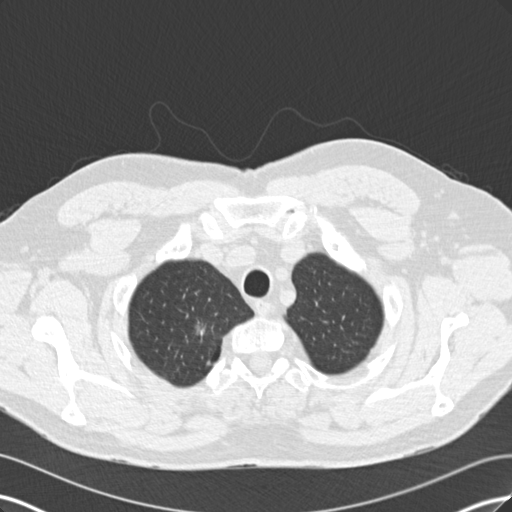
Low-dose screening chest CT, one axial slice; slice 152 of 171 in the series (ordered by position); reconstruction kernel B30f; lung window (W 1500 / L -600 HU); 2 mm slice thickness; 512 × 512 image matrix, field of view 360 × 360 mm.
Annotated regions visible in this slice (expert manual segmentation):
- lesion 1 (tumor, upper lobe of right lung): box from (x=197, y=326) to (x=205, y=336) px